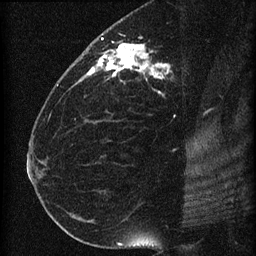
Breast MRI (dynamic contrast-enhanced), one sagittal slice; slice 34 of 60 in the series (ordered by position); dynamic contrast-enhanced series, image 2 of 4 at this slice position (ordered by acquisition); 1.5 T; TE 4.2 ms, TR 22.7 ms; 256 × 256 image matrix, field of view 180 × 180 mm. Patient: female, 35 years. Case-level facts recorded for this patient, not image findings: setting: breast cancer imaged before/during neoadjuvant chemotherapy; receptor status: HR-positive, HER2-negative.
Outlined on this slice (semi-automatic segmentation, software-assisted and operator-edited):
- analysis volume of interest (the breast-tissue region the enhancement analysis was run in; not a lesion): bounding box <69,27,199,112> (left, top, right, bottom; pixels)
- tumour enhancement mask (voxels above the 90 % enhancement threshold inside the analysis volume of interest): <82,37,169,93>